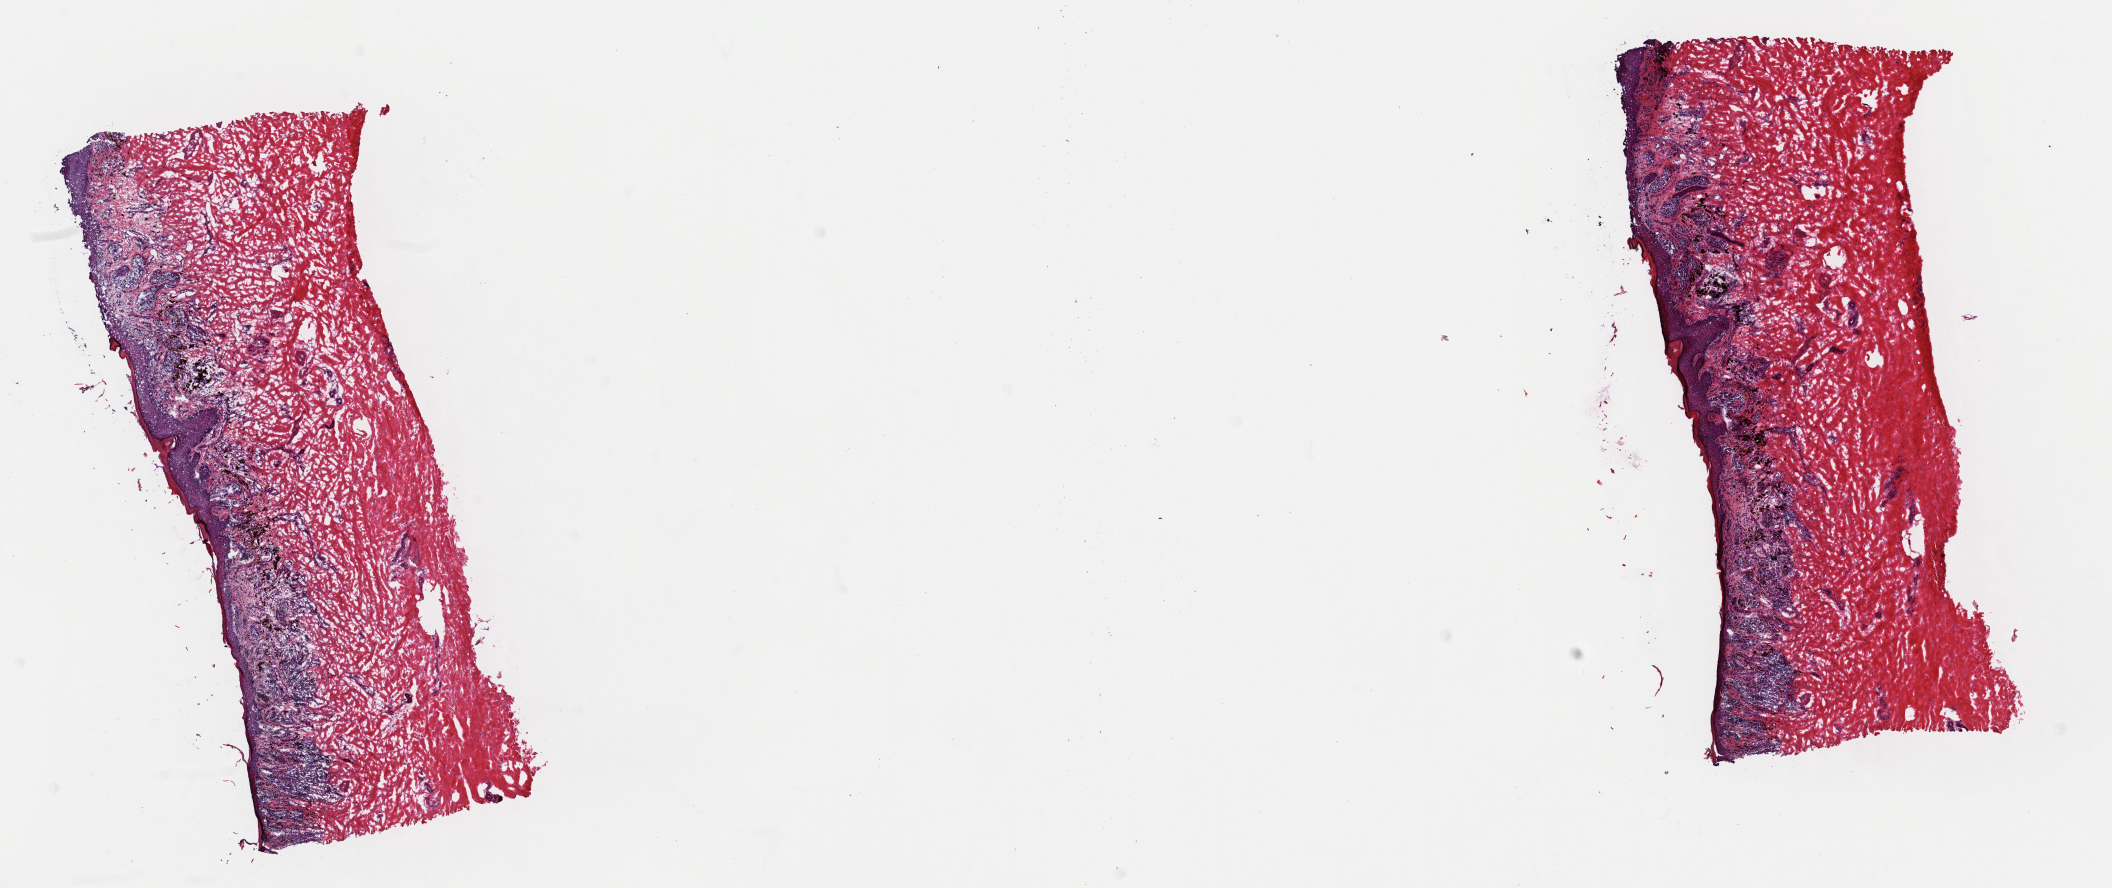
Digitized H&E-stained tissue section (whole slide), low-resolution overview of the scanned area, about 16.7 x 7.0 mm; frozen section; primary tumour sample from the skin. Female patient; age at initial diagnosis 53 years. Slide review estimates, as recorded: tumour cells 60%, tumour nuclei 60%, normal cells 8%, stromal cells 32%, necrosis 0%. Inflammatory infiltration, as recorded: lymphocyte infiltration 12%, monocyte infiltration 2%, neutrophil infiltration 1%.
* diagnosis: Malignant melanoma, NOS
* AJCC pathologic stage: IIC (7th edition)